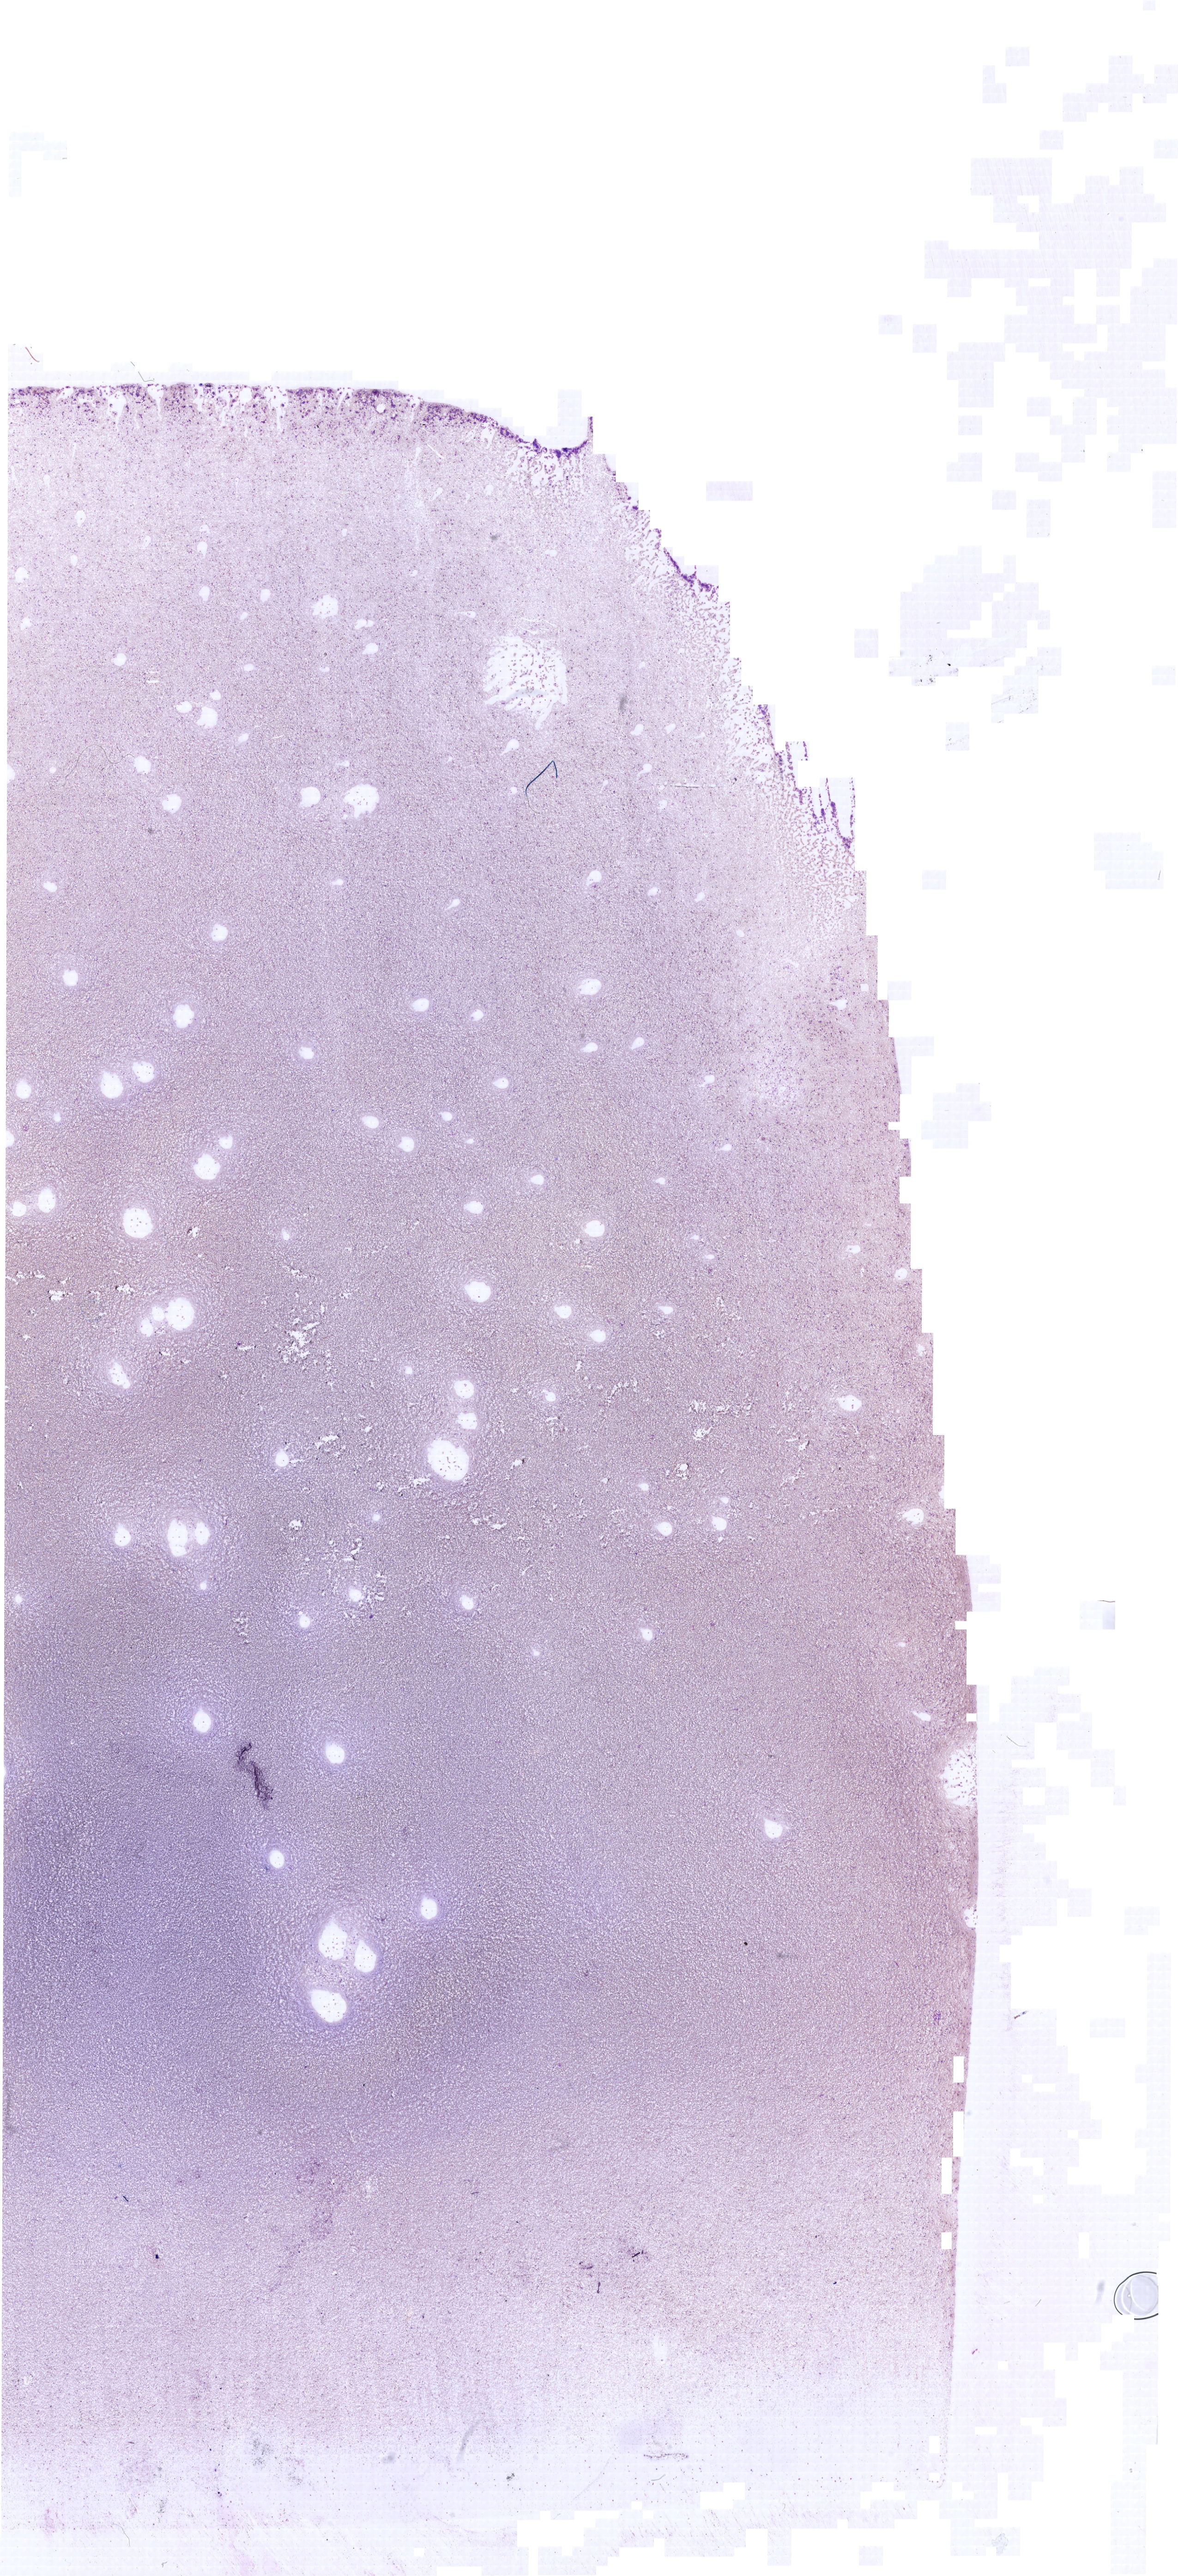
Bone marrow aspirate smear, May-Grünwald-Giemsa (MGG) stain, whole-slide image, a low-resolution overview of the entire scanned area, about 19.9 x 43.6 mm. Female patient.
Diagnosis: B Acute Lymphoblastic Leukemia.